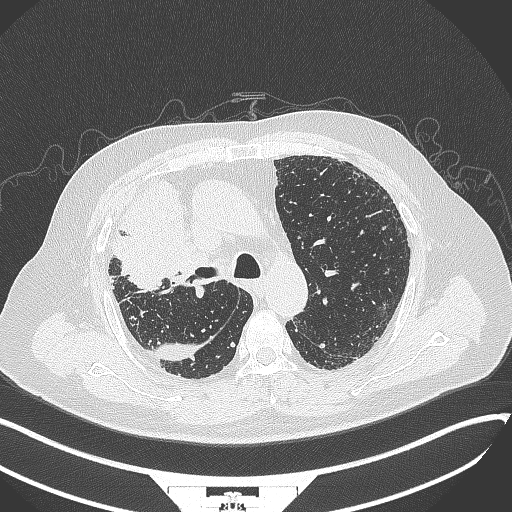
Chest CT, one axial slice; position 246 of 384 along the scan axis; lung window (W 1500 / L -600 HU); 512 × 512 image matrix, field of view 400 × 400 mm. Patient: male, 69 years. From the clinical record (not read from this slice): clinical TNM (as recorded): T4 N3 M1.
Annotated regions visible in this slice (rectangle marked by the reading radiologist):
- lung tumour (recorded histology: adenocarcinoma): bounding box <104,176,196,296> (left, top, right, bottom; pixels)